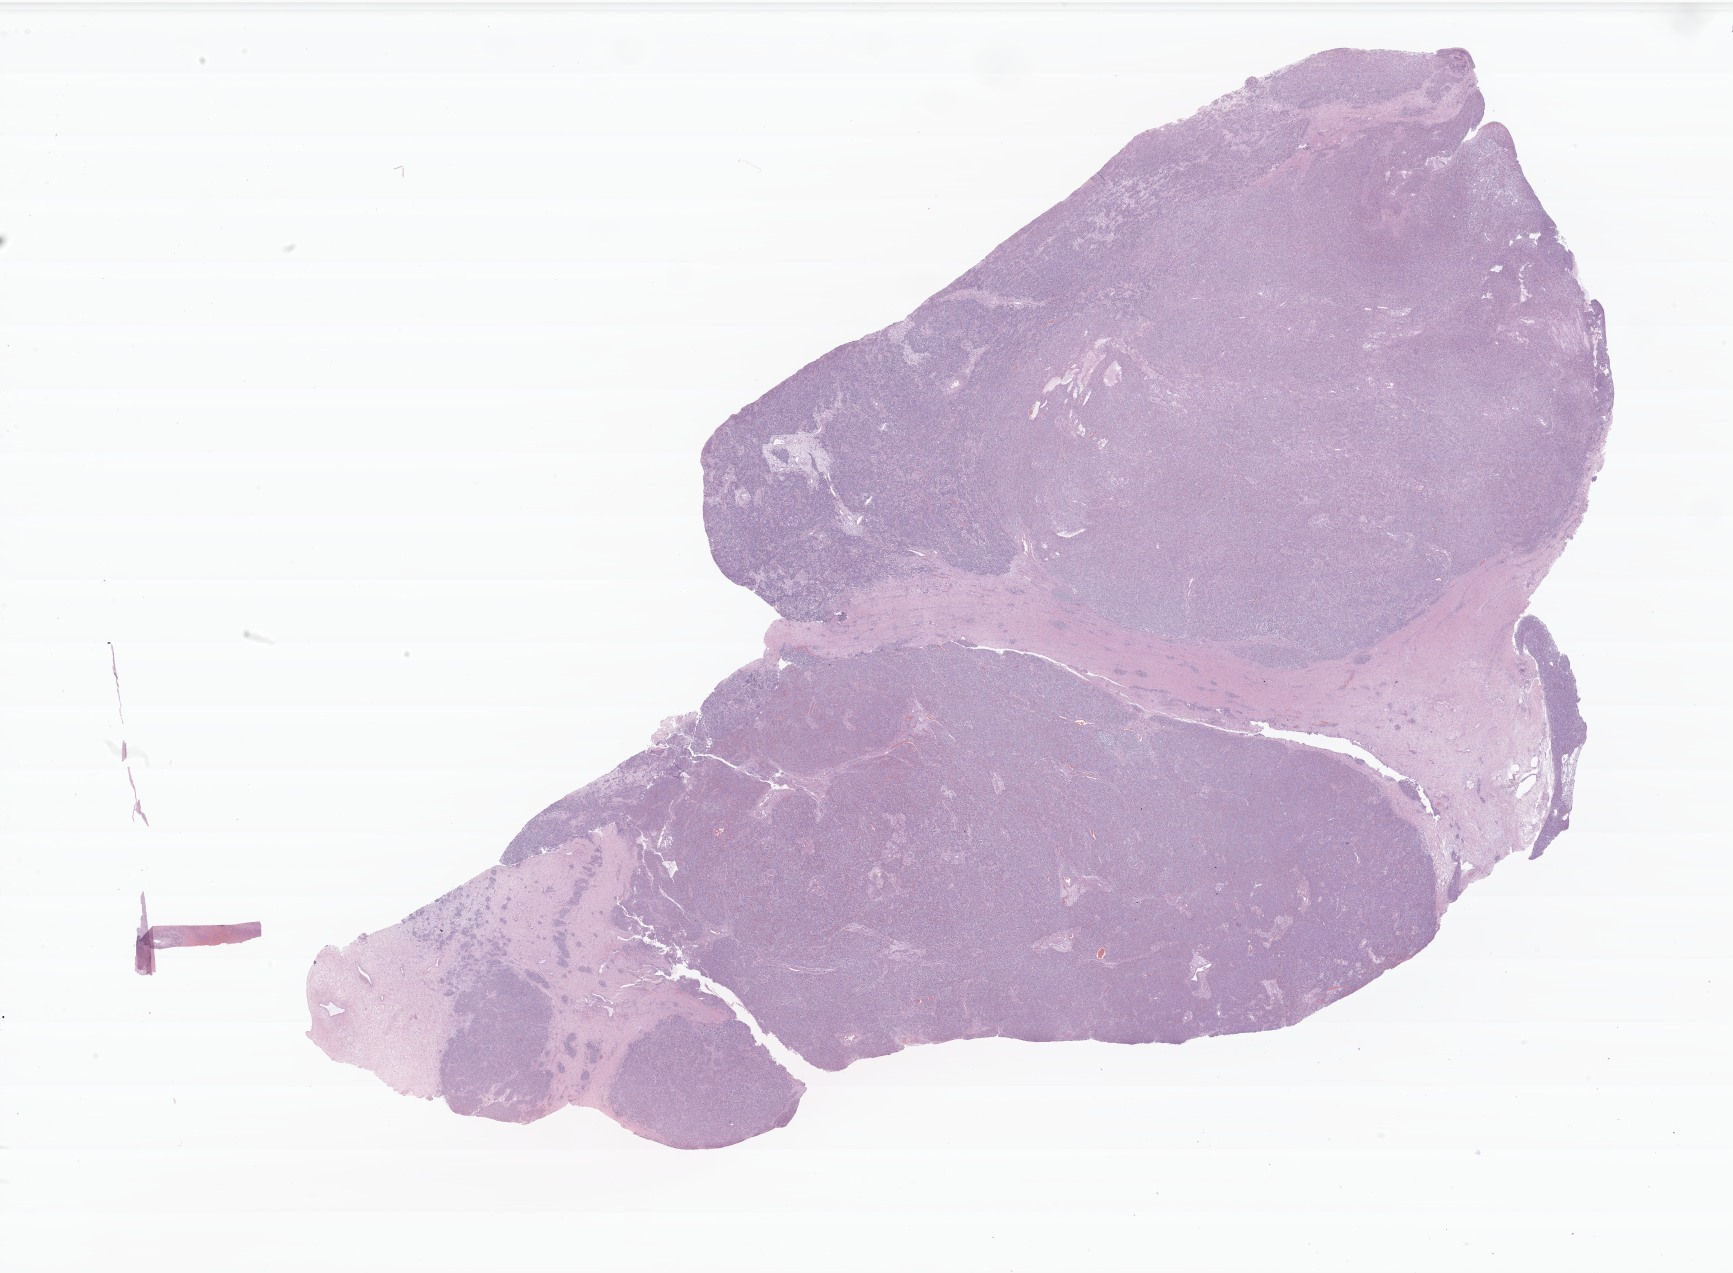
Digitized H&E-stained section of tumor tissue from the ovary — whole scanned area (about 29.2 x 21.4 mm) shown as a low-resolution overview; formalin-fixed, paraffin-embedded (FFPE) tissue. Patient female; age 192 months (16 years).
Diagnosis (ICD-O-3 morphology term): Sertoli cell tumor, NOS.